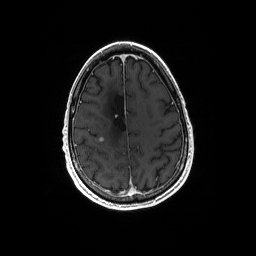
Brain MRI from a brain-tumour surgery series, one axial slice. Position 52 of 192 along the scan axis. T1-weighted post-contrast. 1 mm slice thickness. 256 × 256 image matrix. From the clinical record (not read from this slice): histopathology: Astrocytoma; WHO grade: 4; IDH mutation: yes.
Annotated regions visible in this slice (expert manual segmentation):
- tumour: bounding box <95,141,104,143> (left, top, right, bottom; pixels)